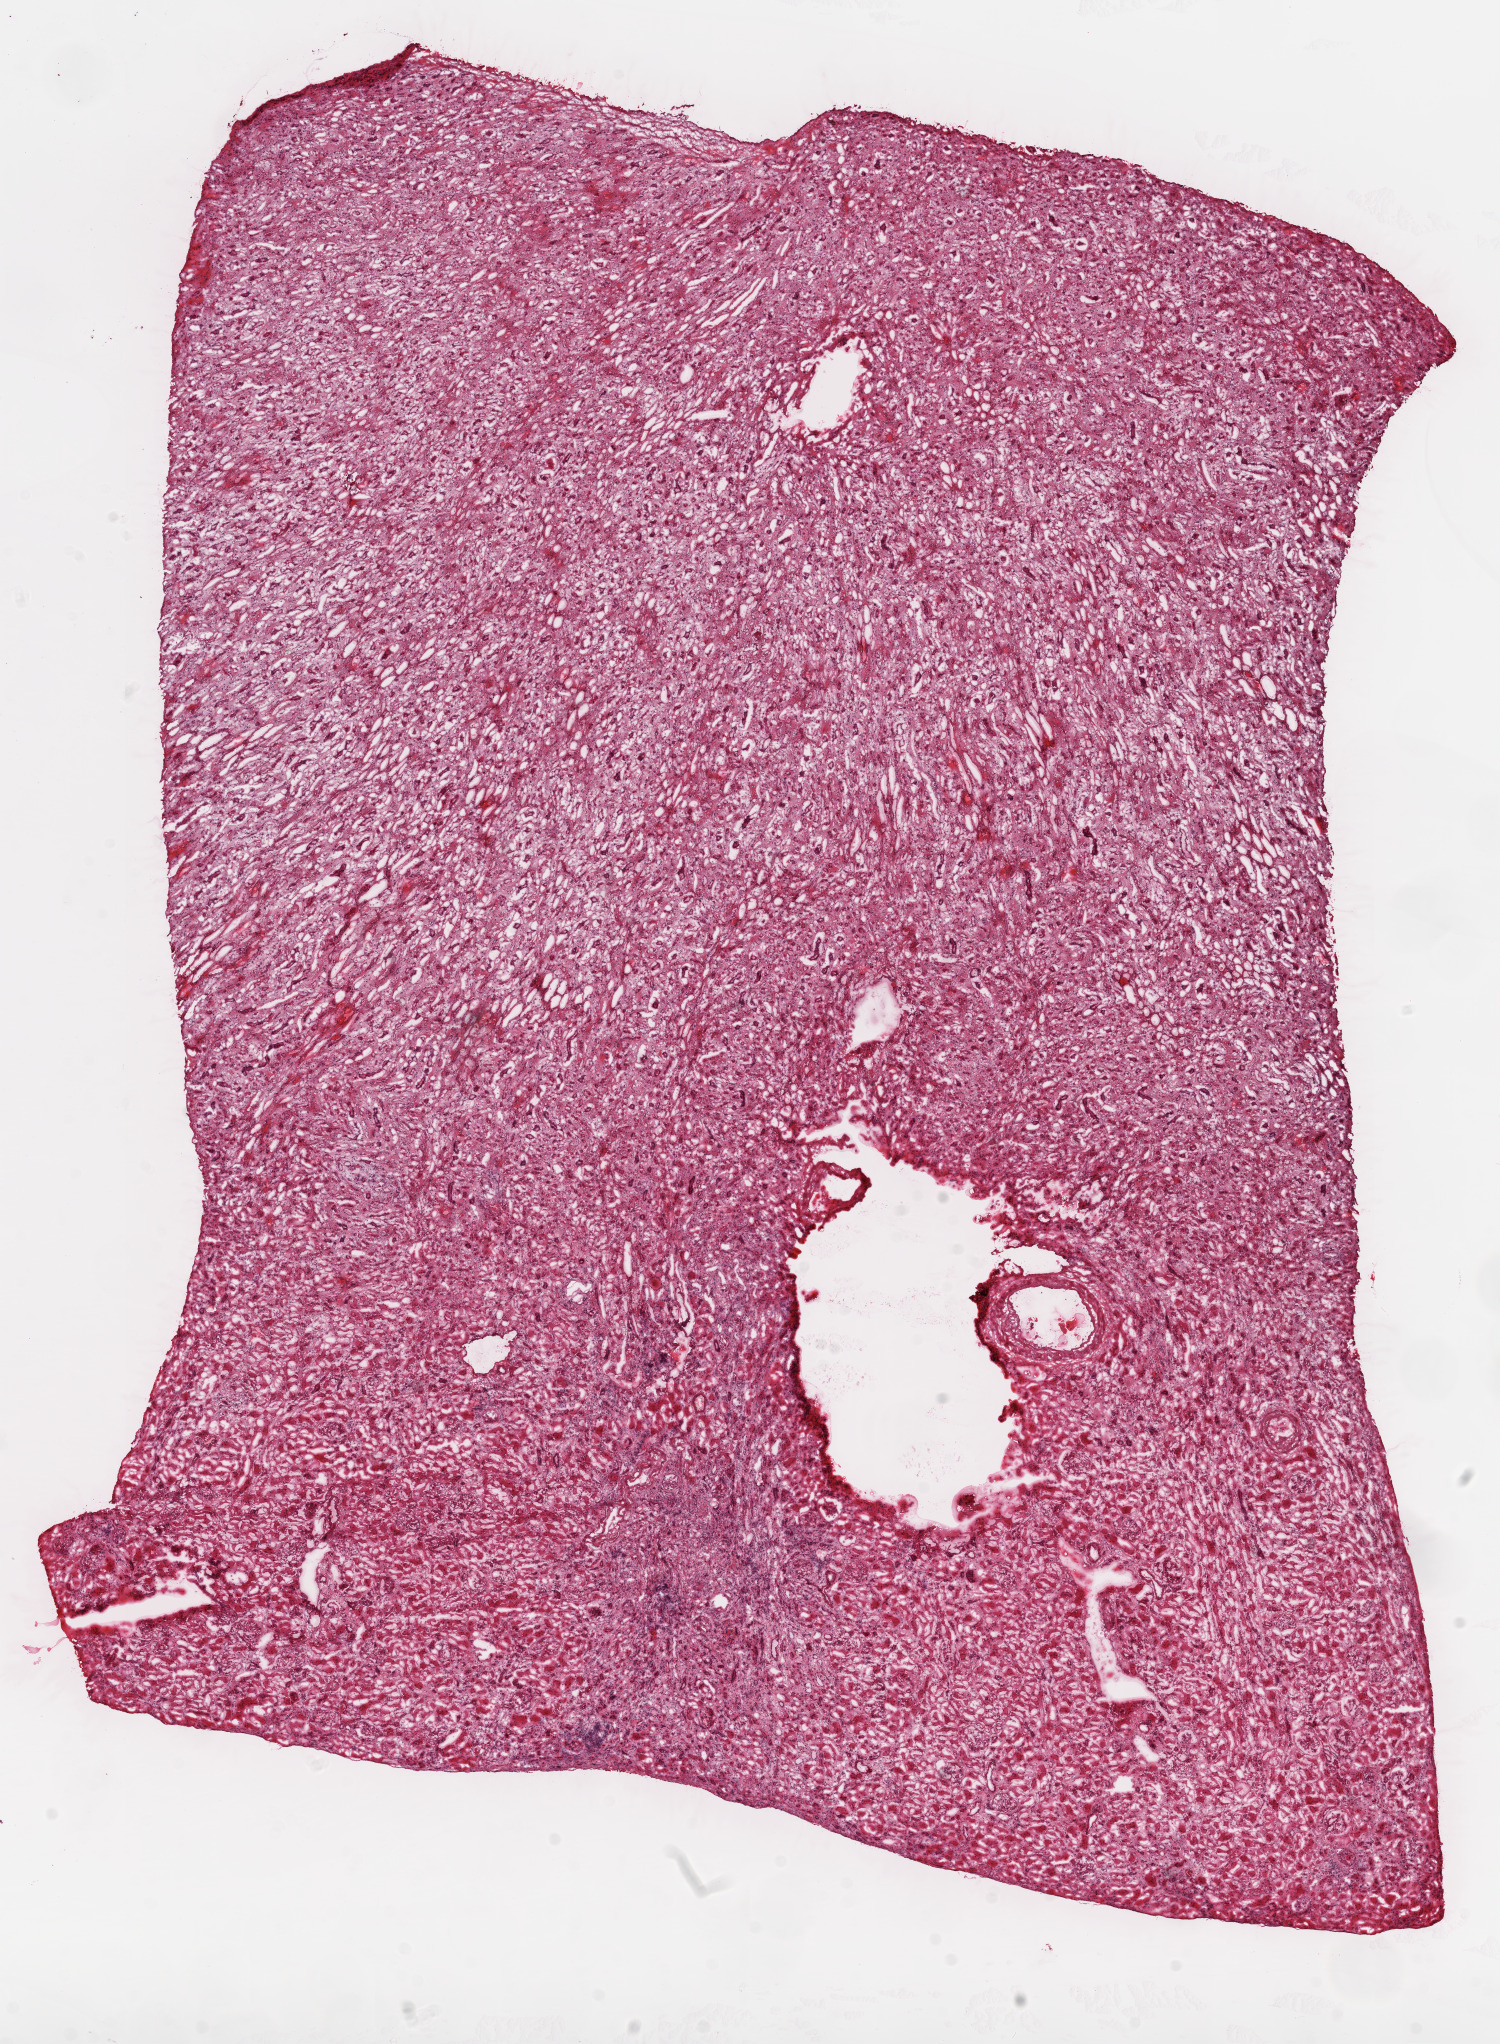
Digitized H&E-stained tissue section (whole slide), whole scanned area (about 12.0 x 16.4 mm) shown as a low-resolution overview; frozen section; kidney, solid tissue normal (non-tumour tissue) sample. Female patient; age at initial diagnosis 65 years.
This section: solid tissue normal (non-tumour) sample from the same patient. Patient diagnosis: Clear cell adenocarcinoma, NOS.